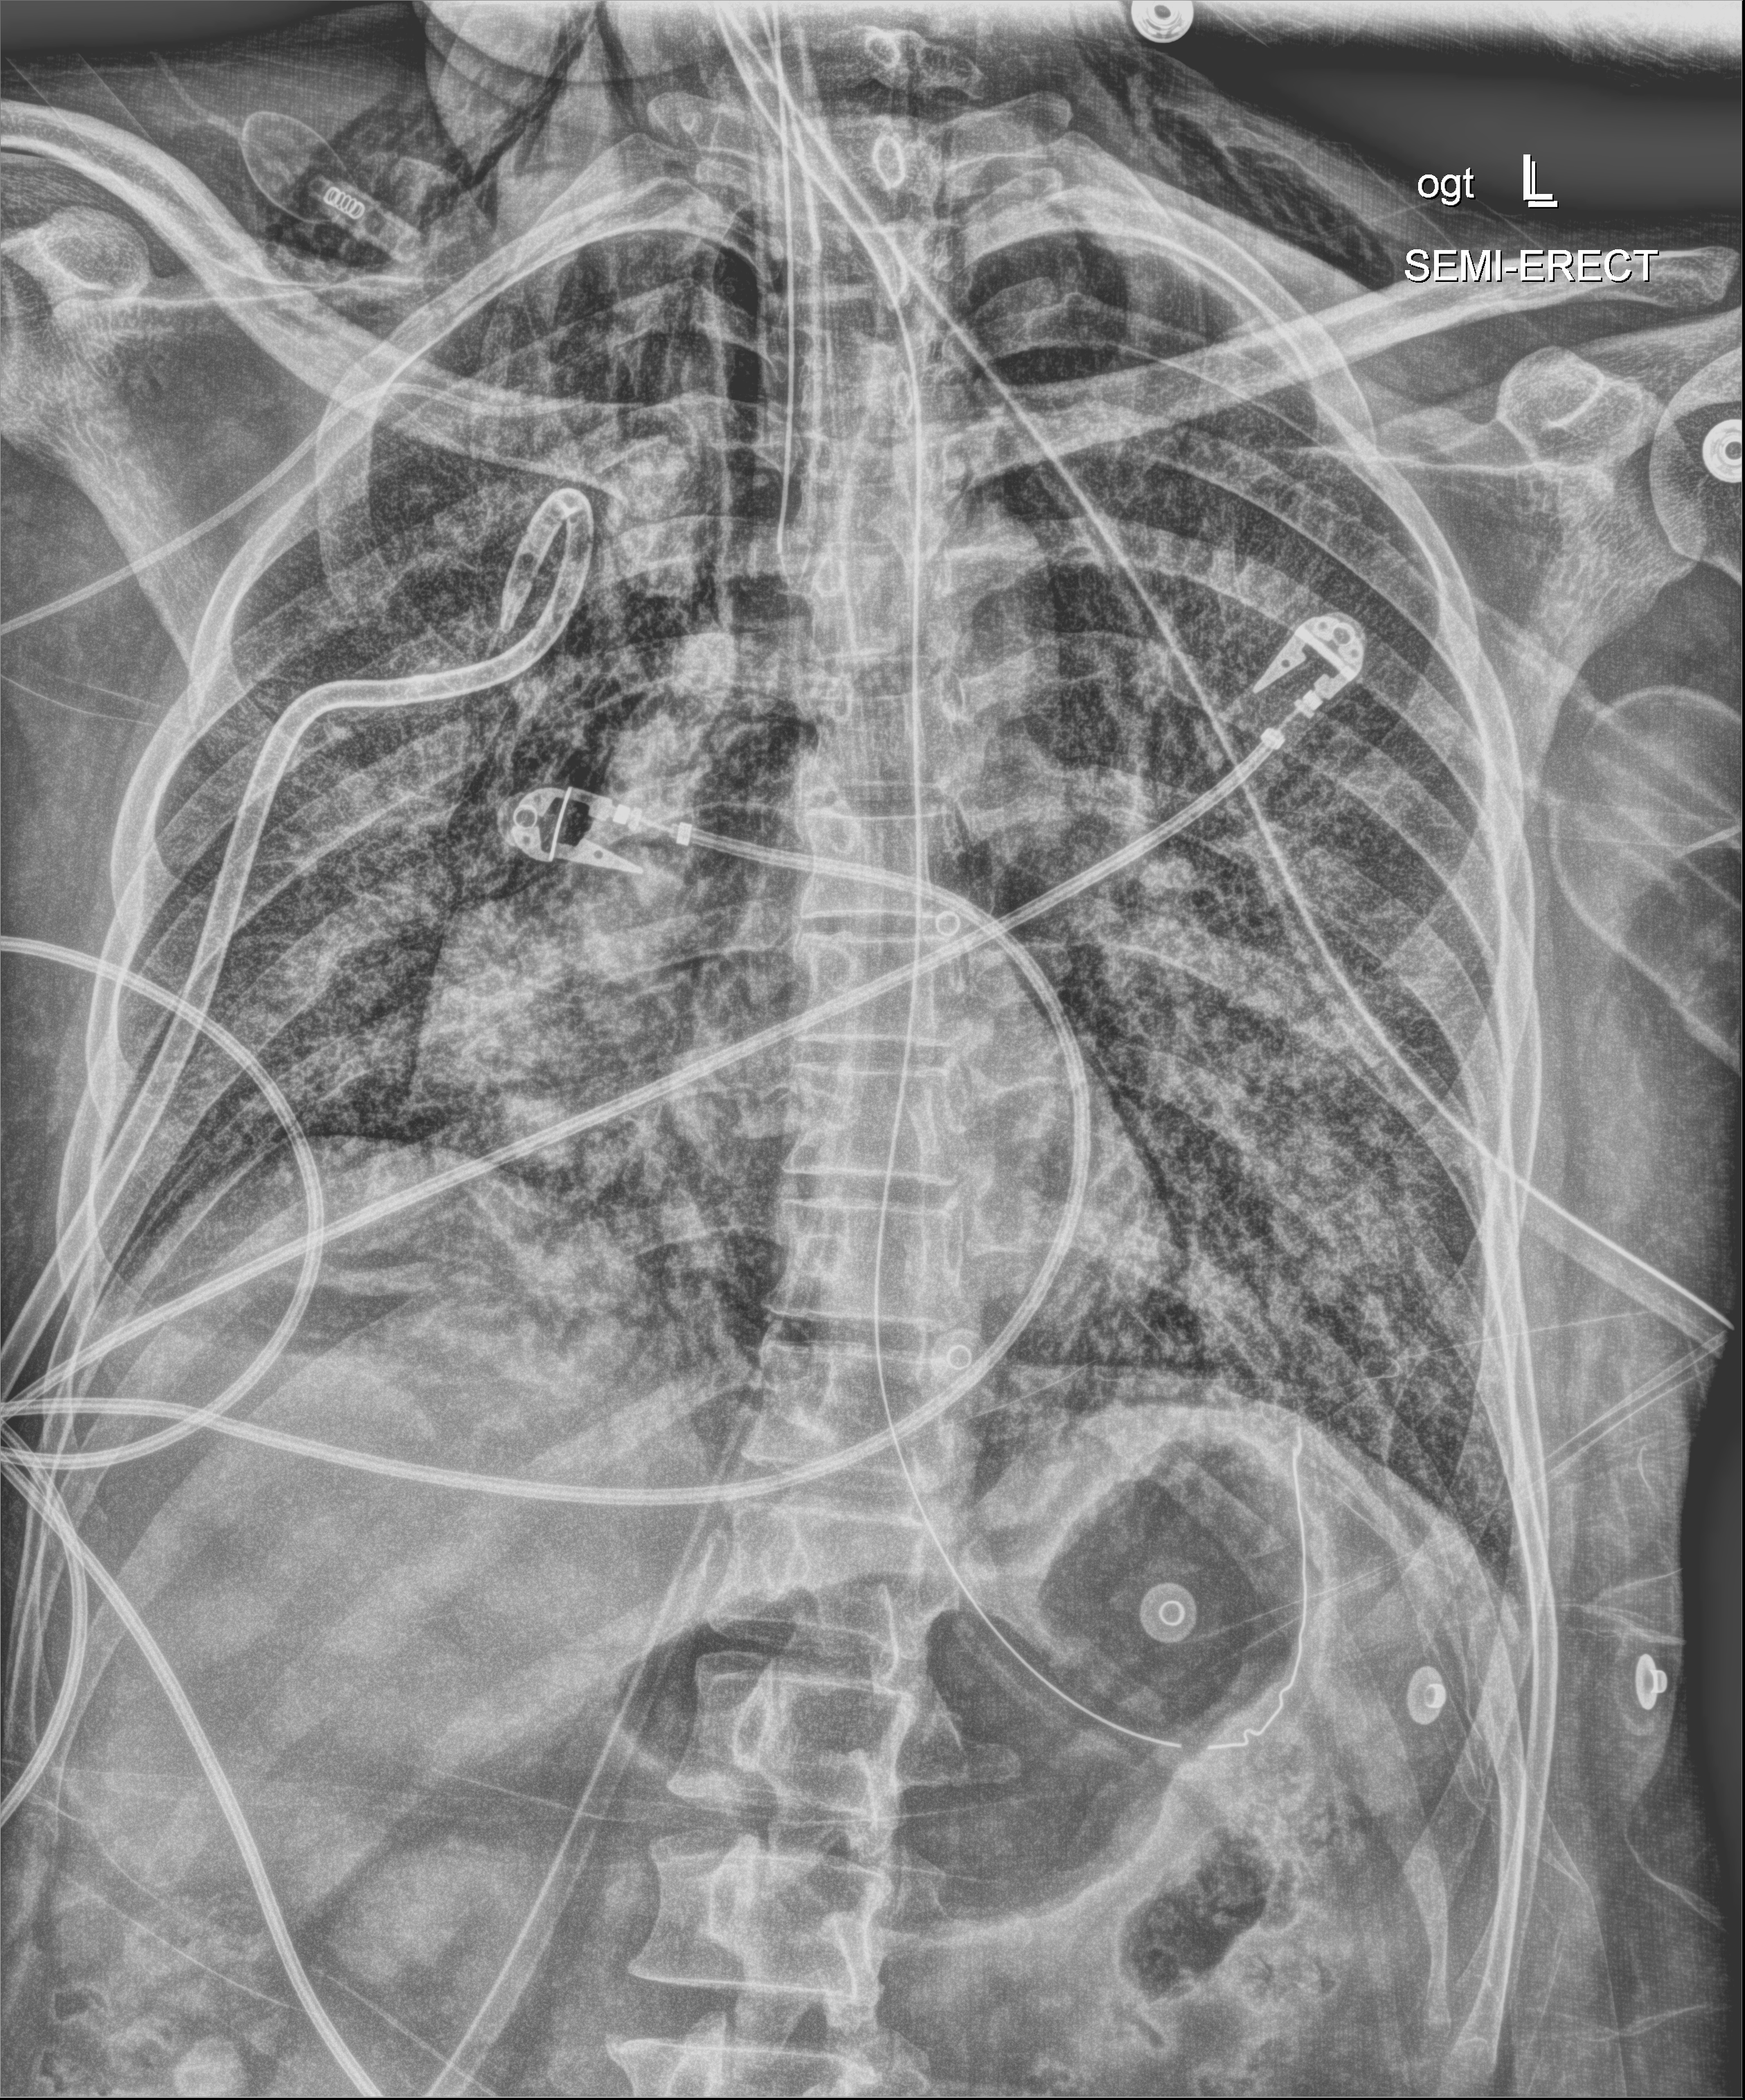
Bedside chest radiograph (digital radiography). Adult patient hospitalised with COVID-19, age 18–59 years.
Admission-level facts for this patient (not findings on this image; timing relative to this image not recorded): length of hospital stay: 41 days.